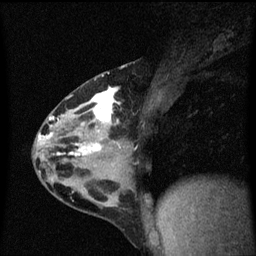
Breast MRI (dynamic contrast-enhanced), one sagittal slice; slice 32 of 60 in the series (ordered by position); dynamic contrast-enhanced series, image 2 of 3 at this slice position (ordered by acquisition); 1.5 T; TE 4.2 ms, TR 8.4 ms; 2 mm slice thickness; 256 × 256 image matrix, field of view 200 × 200 mm. Patient: female, 32 years.
Outlined on this slice (semi-automatically segmented with operator editing):
- analysis volume of interest (the breast-tissue region the enhancement analysis was run in; not a lesion): bounding box (x1, y1, x2, y2) in pixels: (34, 74, 149, 169)
- tumour enhancement mask (voxels above the 70 % enhancement threshold inside the analysis volume of interest): (39, 88, 122, 157)